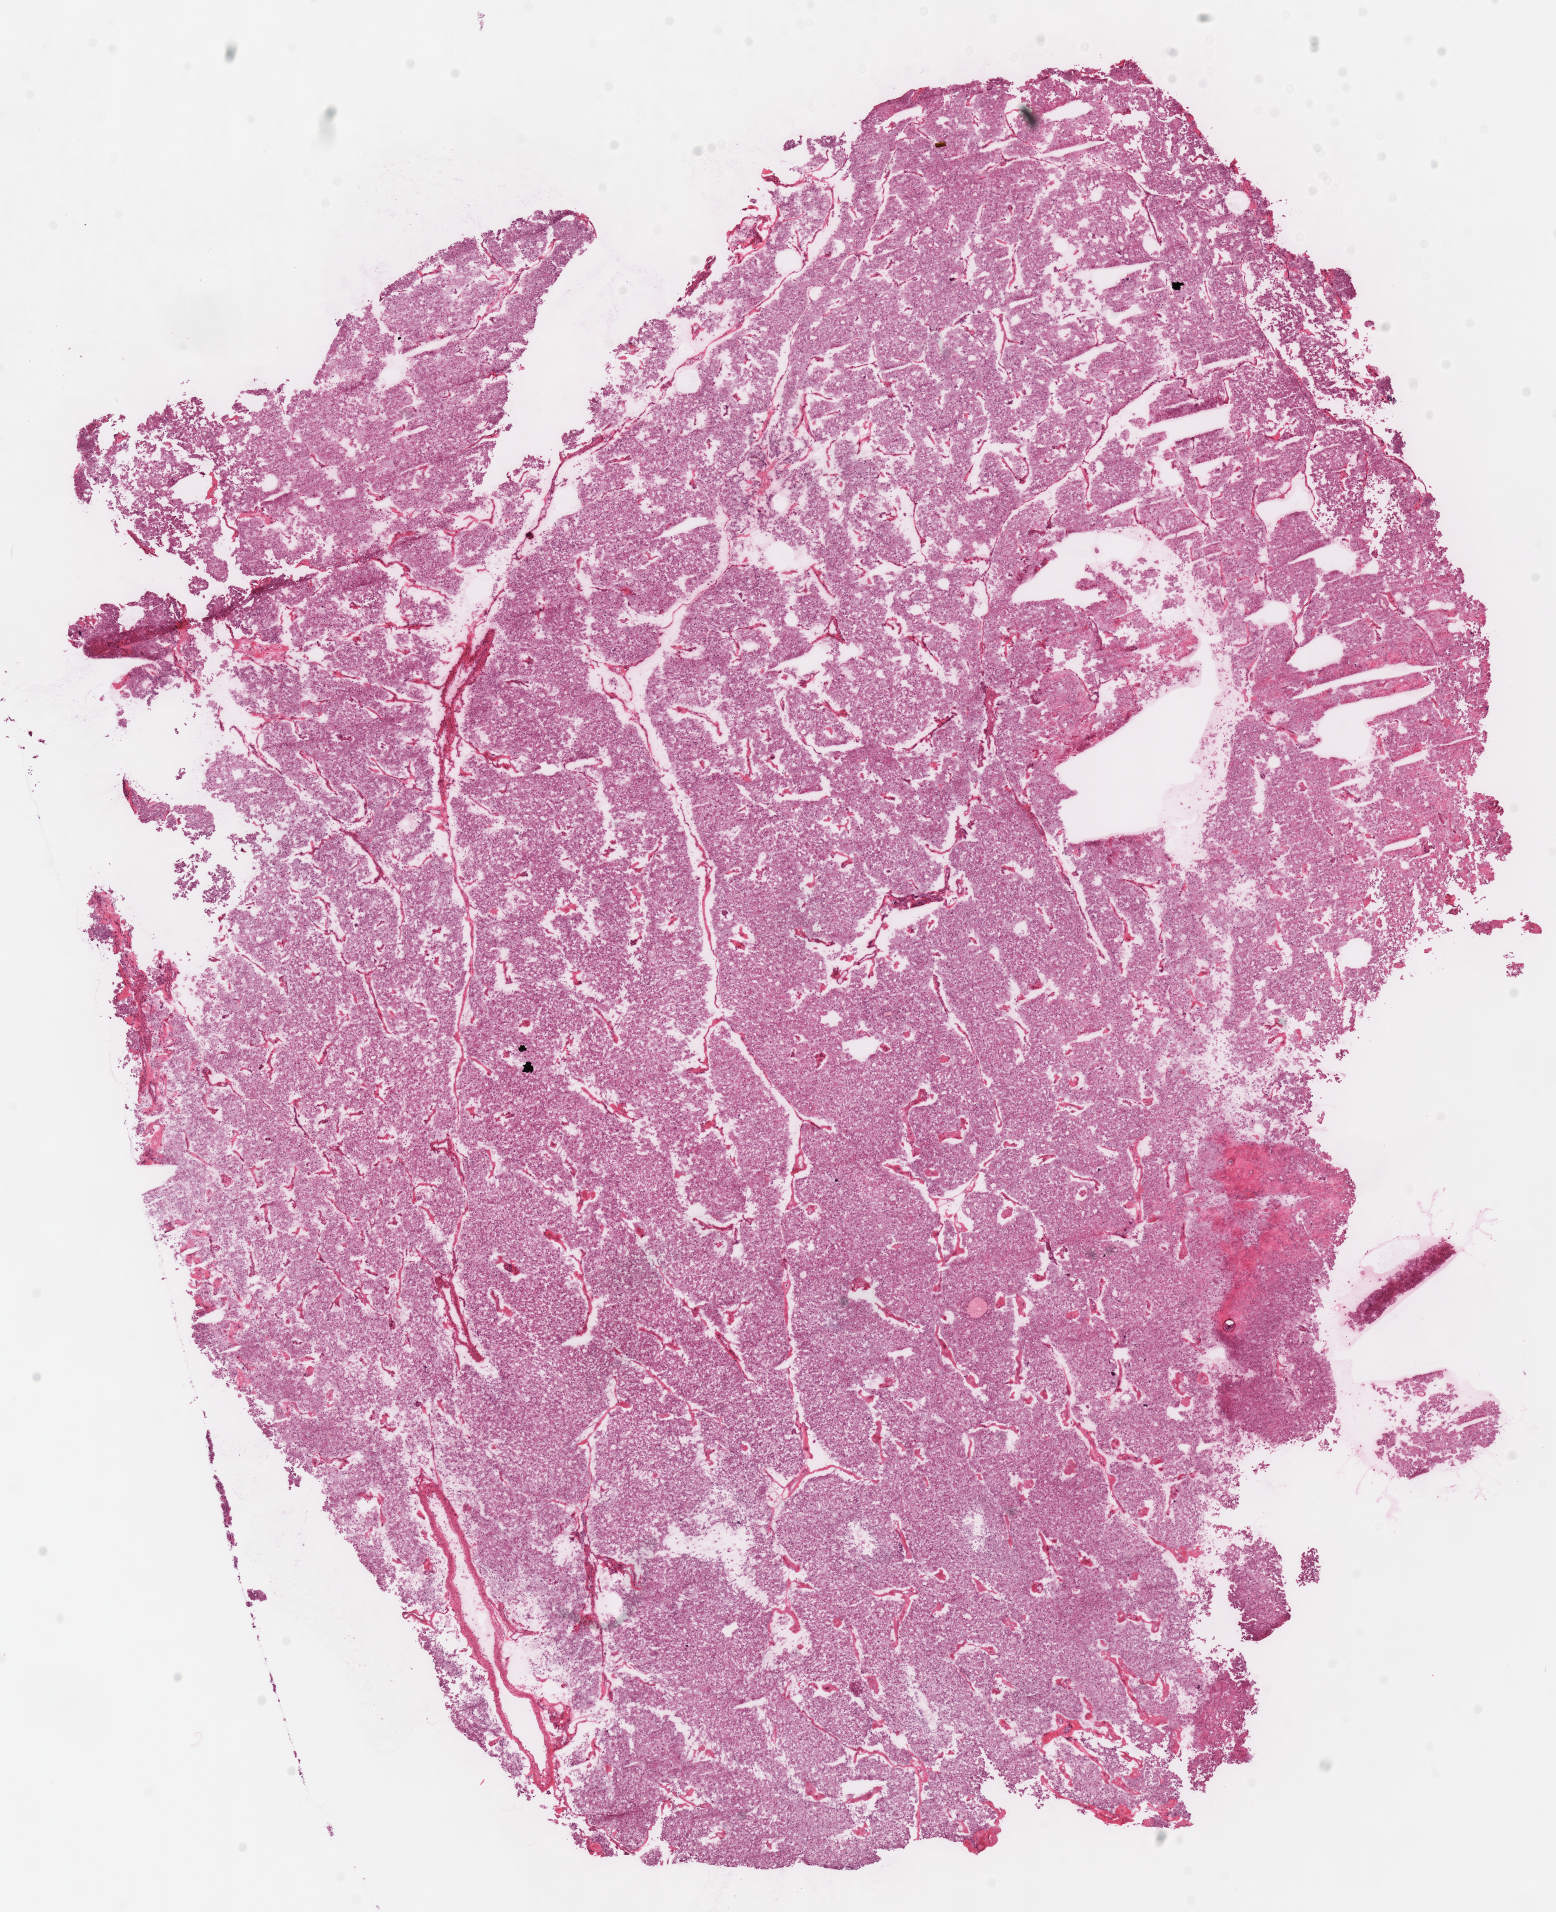
Digitized Hematoxylin and eosin (H&E) stained tissue section (whole slide), a low-resolution overview of the entire scanned area, about 12.2 x 15.0 mm. Frozen section from the top of the tissue portion. Kidney, primary tumour sample. Male patient; age at initial diagnosis 34 years. Composition of this section per pathologist review: tumour cells 95%, tumour nuclei 95%, normal cells 0%, stromal cells 5%, necrosis 0%.
• diagnosis: Renal cell carcinoma, chromophobe type
• lymph nodes positive (case pathology): 0 of 13 examined
• AJCC pathologic stage: II (6th edition)